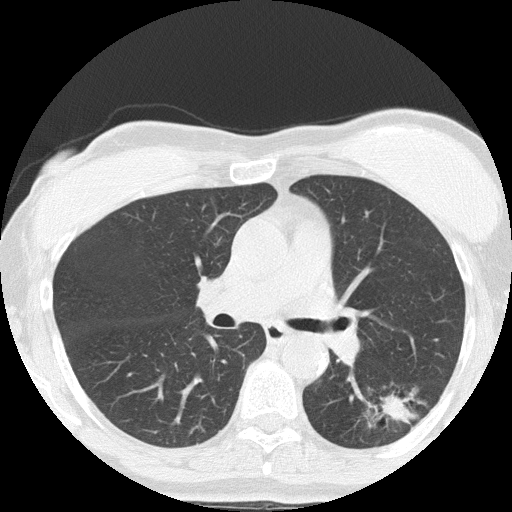
Low-dose screening chest CT, axial slice. Third screening round (two years after baseline). Lung window (W 1500 / L -600 HU). 2 mm slice thickness. Lung (sharp) reconstruction kernel (FC51). Slice 64 of 152 in the series. Female participant, aged 64 years at enrolment. Former smoker at enrolment.
- Lesion marked by an expert reader, box from (x=357, y=375) to (x=445, y=447) px.
- The screening reader recorded 3 non-calcified nodules or masses ≥4 mm on this exam (right upper lobe, left lower lobe, right middle lobe); which of them this box marks is not recorded.
- Participant outcome: lung cancer diagnosed 212 days after this screen — adenocarcinoma, NOS, left lower lobe, moderately differentiated (G2), stage IA (AJCC 6th edition), 17 mm at pathology.